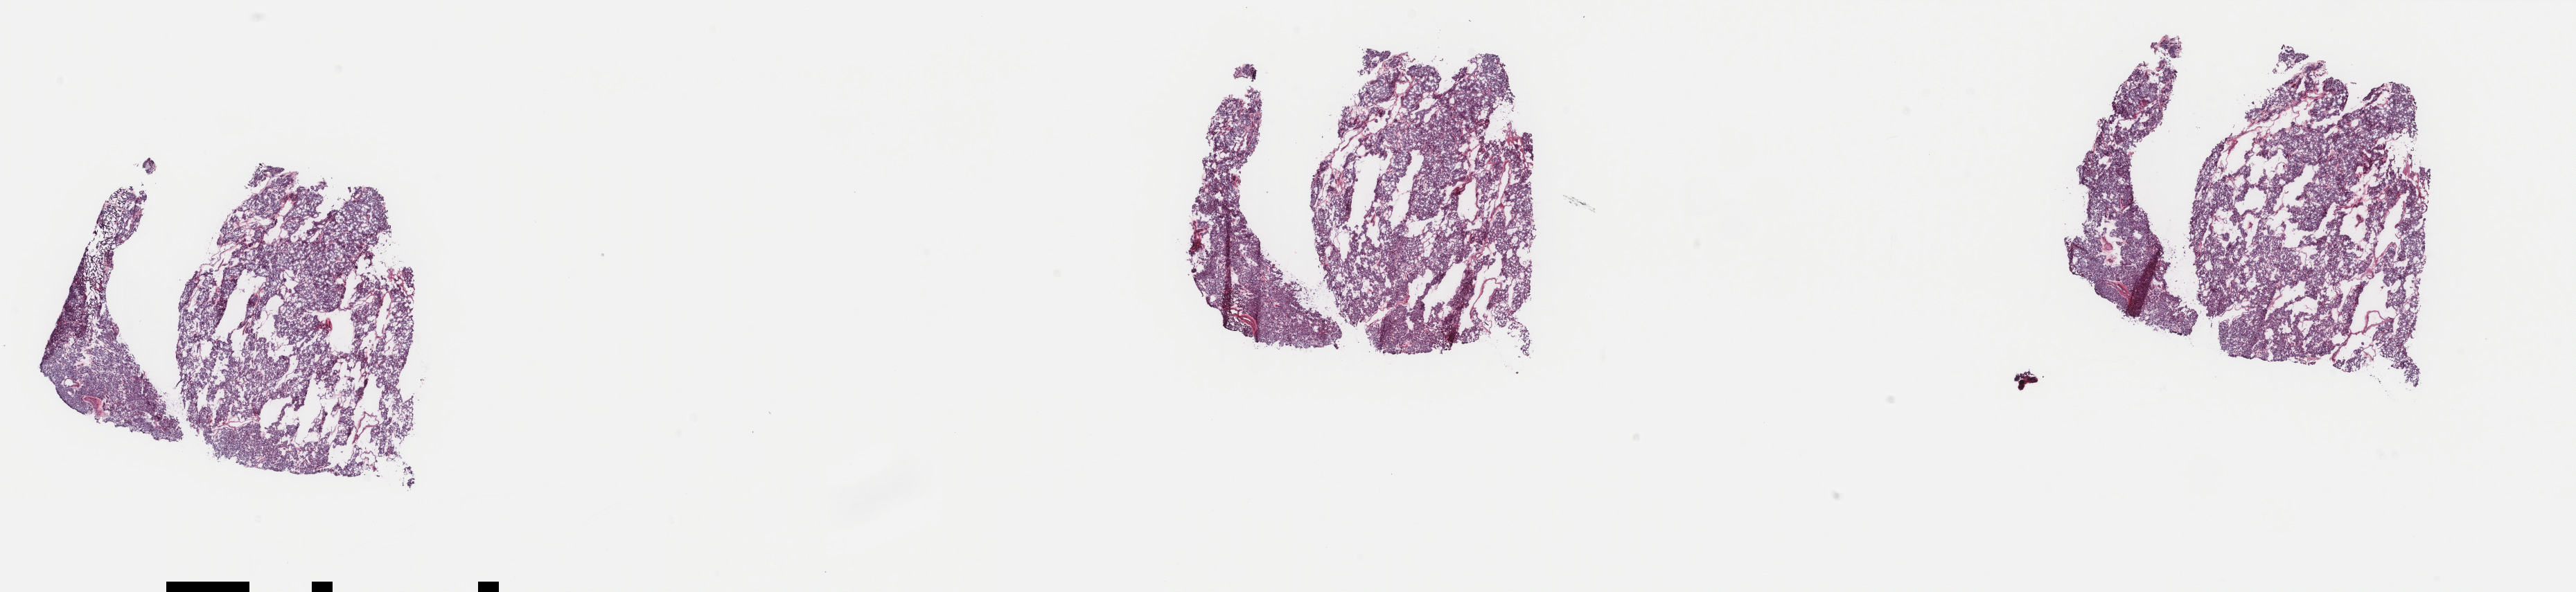
H&E whole-slide image, a low-resolution overview of the entire scanned area, about 29.5 x 6.8 mm (acquisition: 40x scan); frozen section from the top of the tissue portion; primary tumour sample from the connective, subcutaneous and other soft tissues. Patient: male, age at initial diagnosis 53 years. Slide review estimates, as recorded: tumour cells 90%, tumour nuclei 95%, normal cells 0%, stromal cells 10%, necrosis 0%. Inflammatory infiltration, as recorded: lymphocyte infiltration 0%, monocyte infiltration 0%, neutrophil infiltration 0%.
Diagnosis: Paraganglioma, NOS (connective, subcutaneous and other soft tissues of thorax).